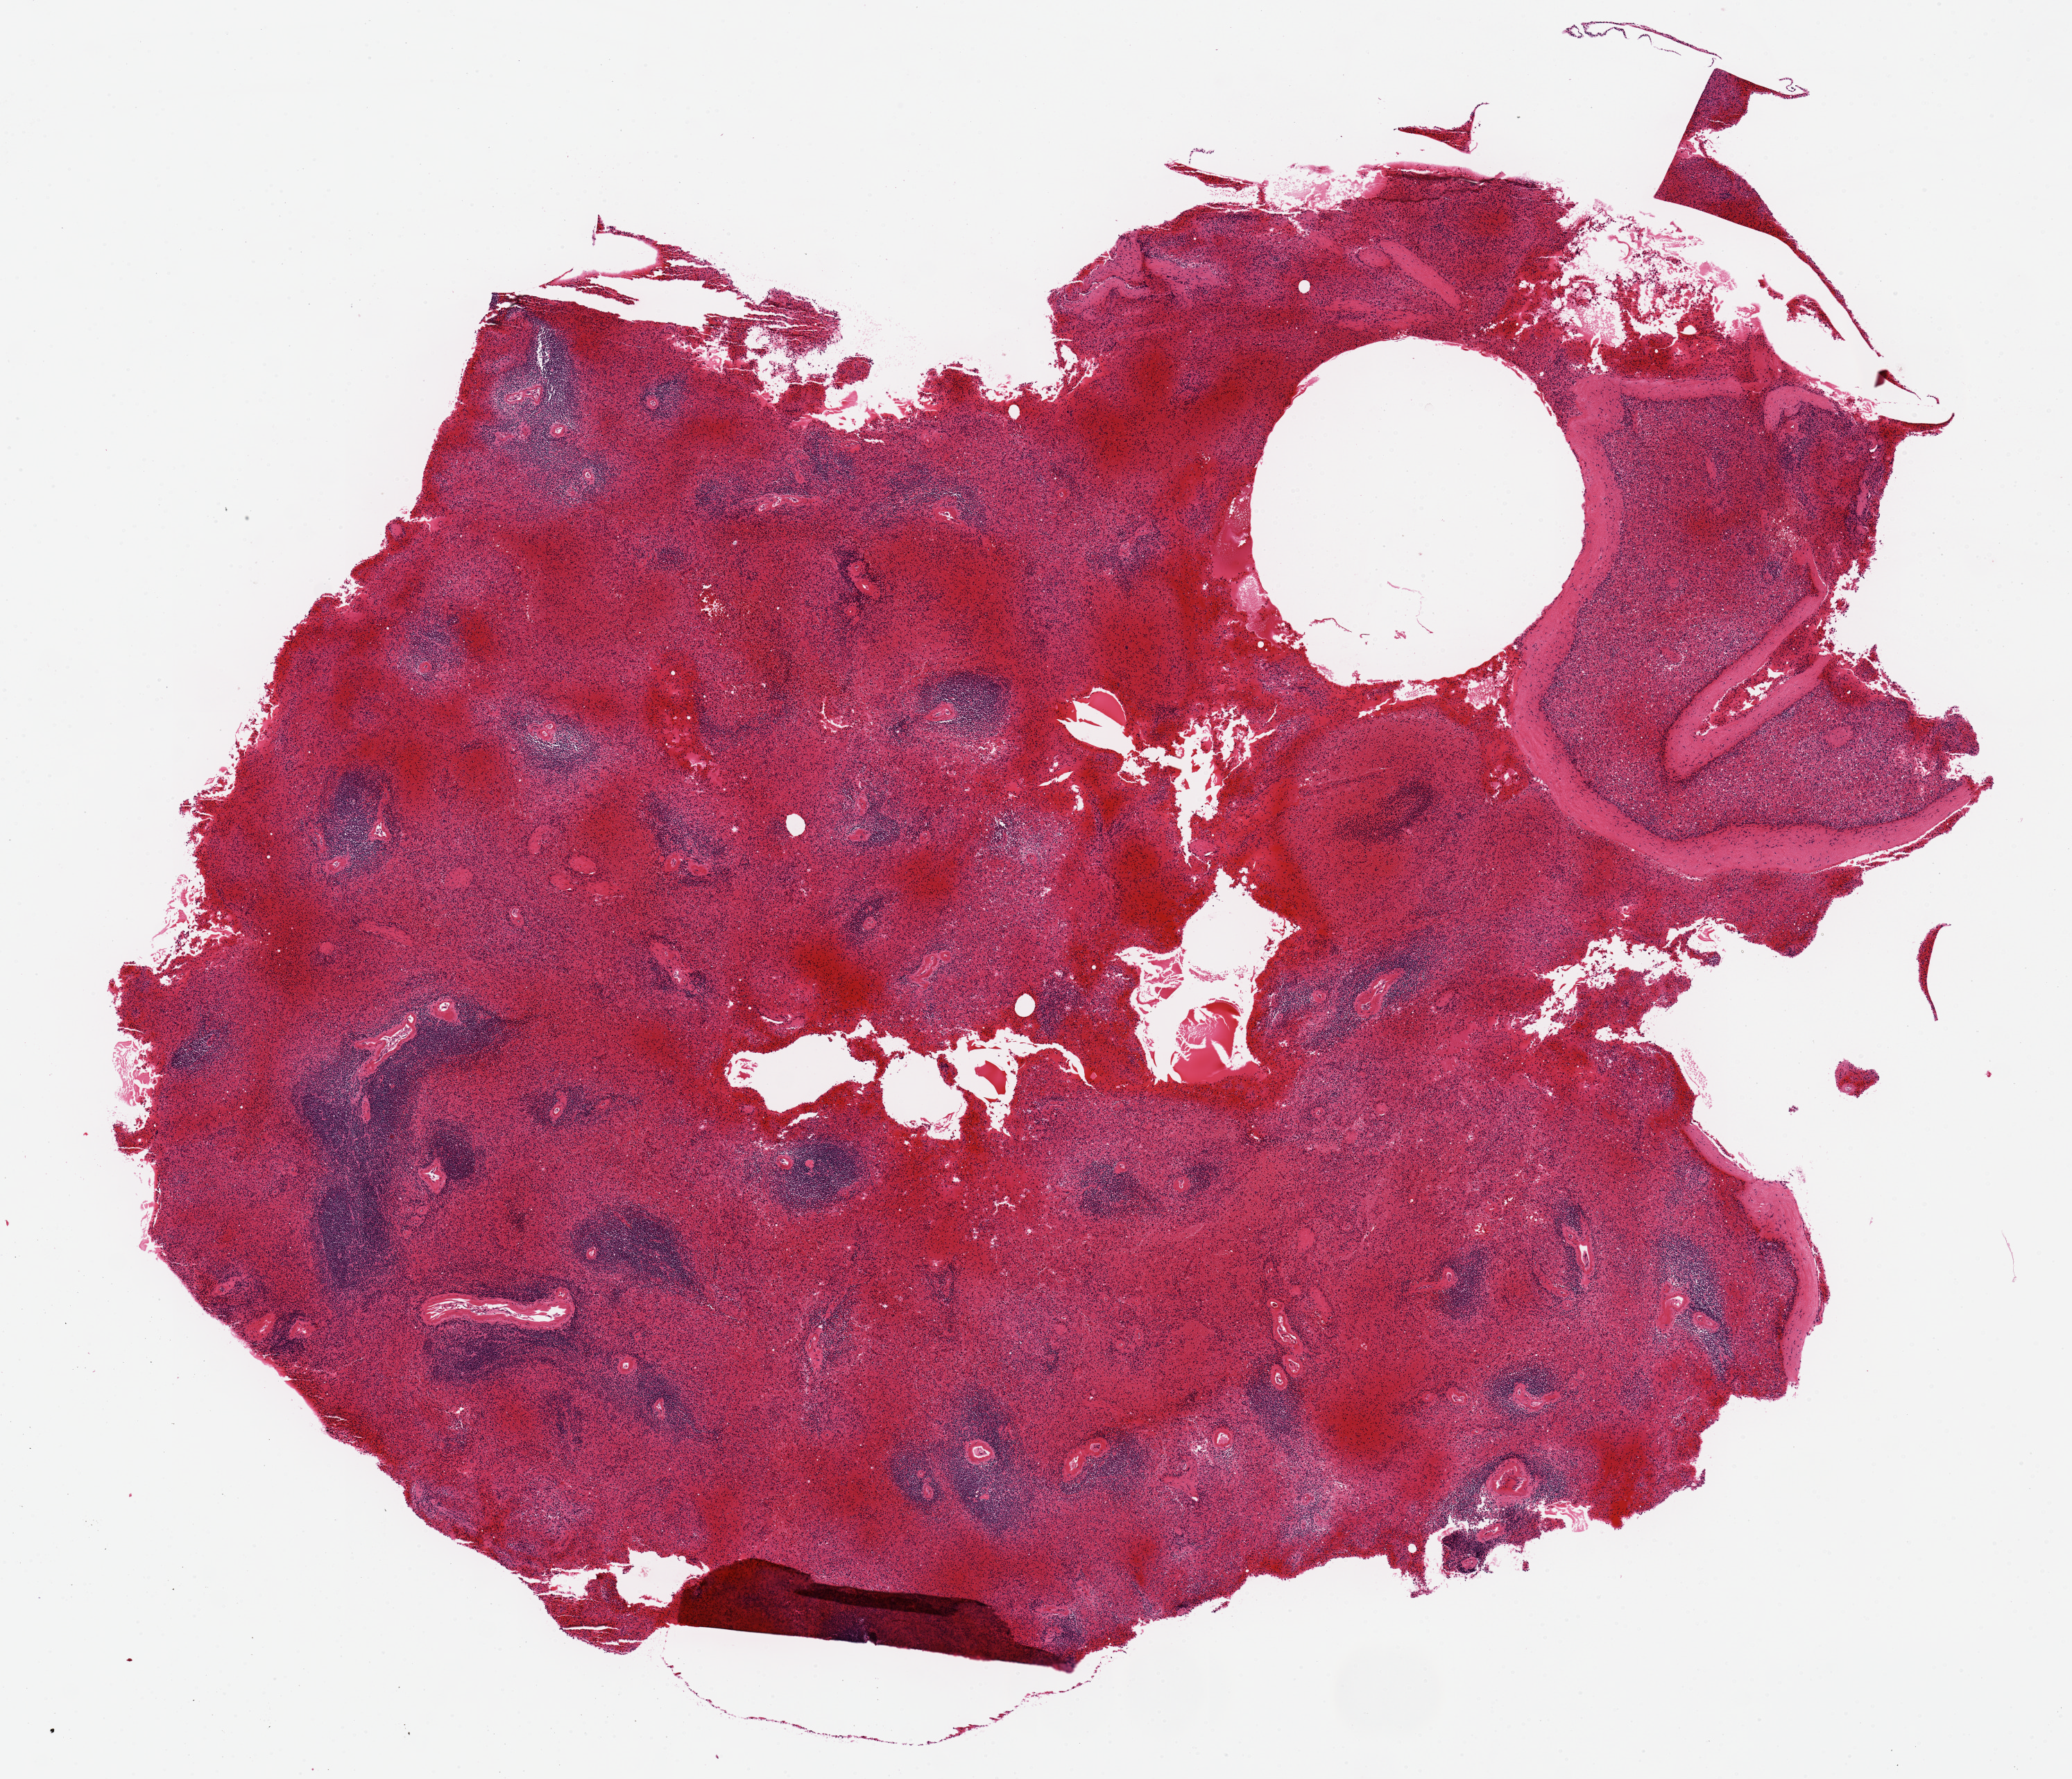
Digitized hematoxylin and eosin (H&E)-stained section, whole scanned area (about 11.8 x 10.1 mm, slide scanned at 20x) shown as a low-resolution overview; PAXgene-fixed, paraffin-embedded tissue; sampled site (target tissue): spleen; tissue donor sample. Donor sex: male.
Pathologist's review note for this sample: moderate congestion; central holes.